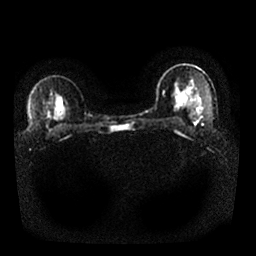
Breast MRI, one axial slice. Position 17 of 25 along the scan axis. Diffusion-weighted series; image 2 of 4 stored at this slice position (different b-values; order by instance number). 1.5 T. 4 mm slice thickness. 256 × 256 image matrix, field of view 340 × 340 mm. Female patient.
Structures marked on this image (expert manual segmentation):
- tumour on diffusion-weighted imaging: bounding box (x1, y1, x2, y2) in pixels: (194, 118, 201, 125)